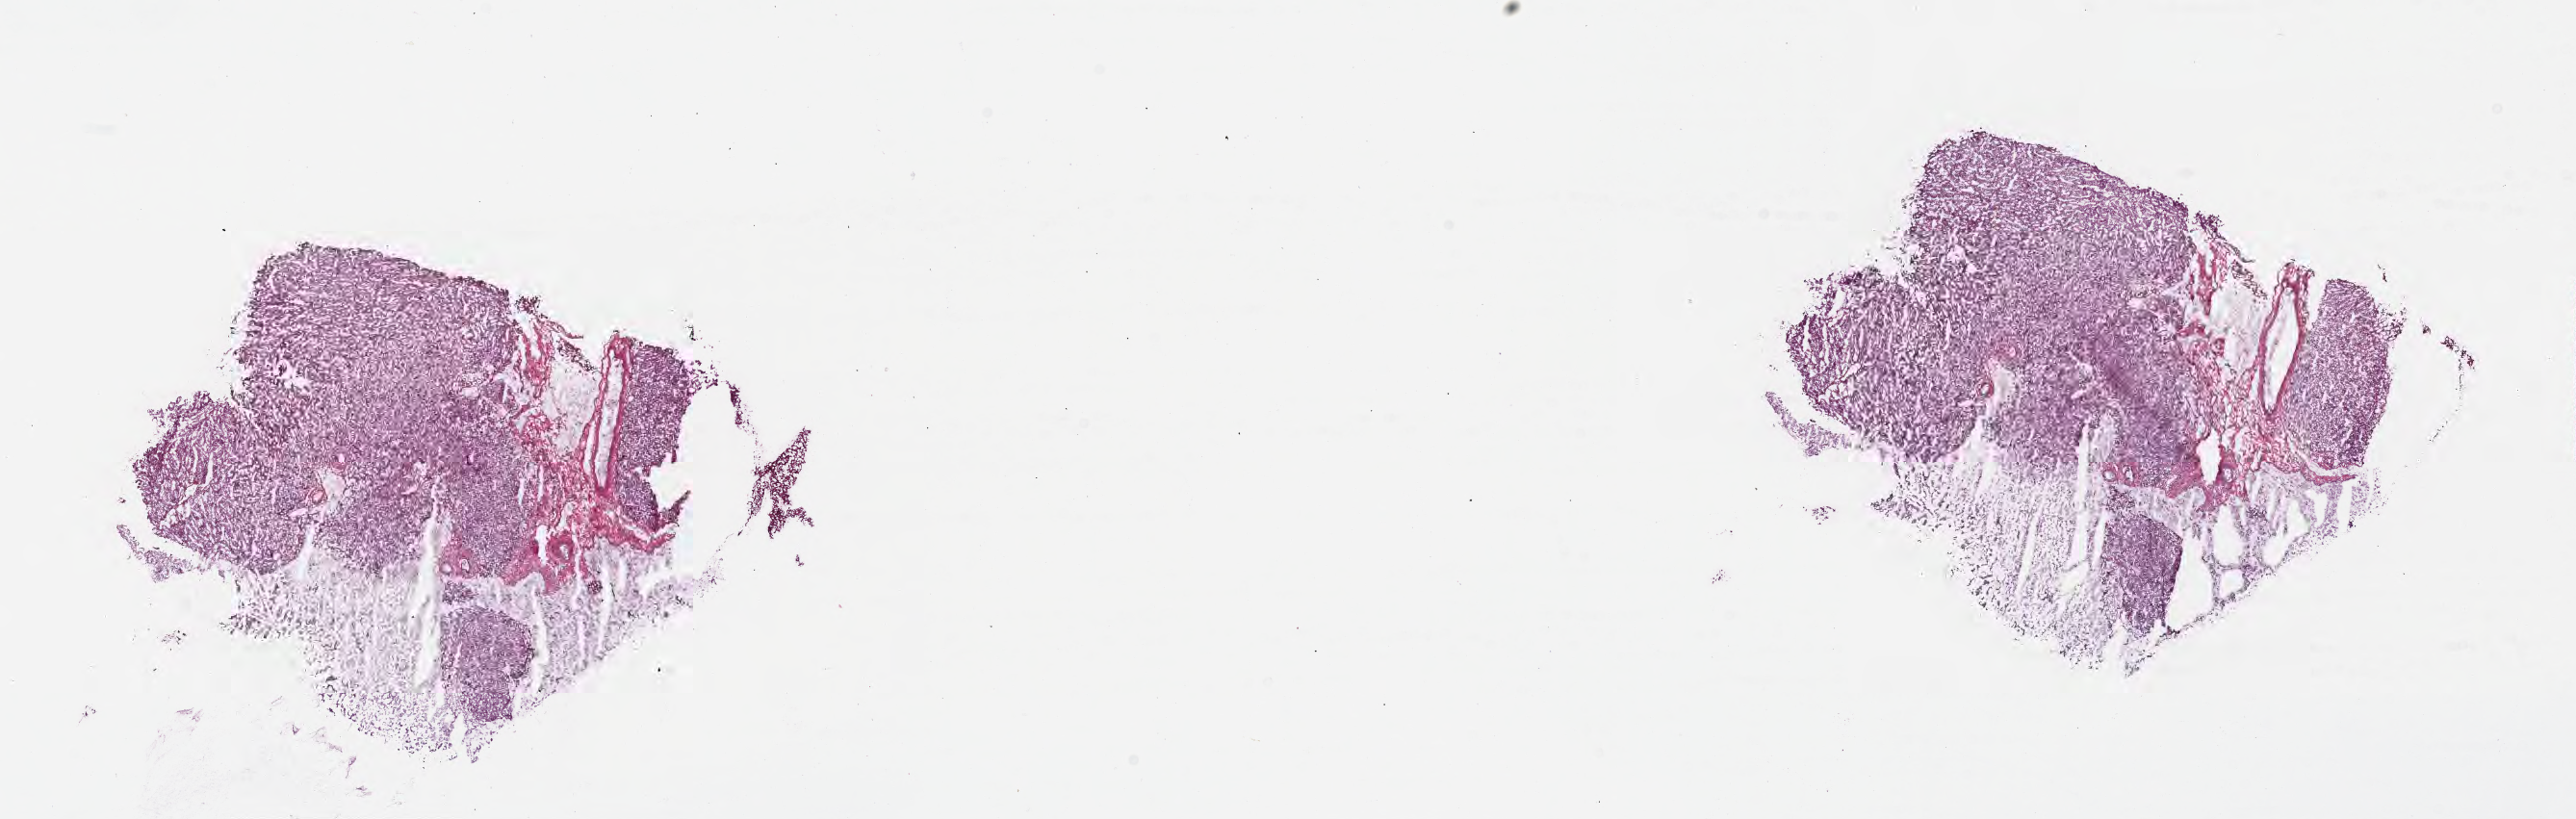
Digitized hematoxylin and eosin (H&E)-stained section — low-resolution overview of the scanned area, about 21.6 x 6.9 mm; frozen section (tissue freezing medium); non-tumor (normal tissue) sample from a patient with adenocarcinoma, NOS; anatomic site: liver. Patient: female, age at initial diagnosis 51 years. Composition of this section per pathologist review: tumor cells 0%, tumor nuclei 0%, stromal cells 33%, necrosis 0%, normal cells 67%. Inflammatory infiltration, as recorded: lymphocyte infiltration 1%, monocyte infiltration 1%, neutrophil infiltration 0%.
This section: non-tumor tissue sample; the patient's diagnosis is given above. Section: bottom of the tissue portion.